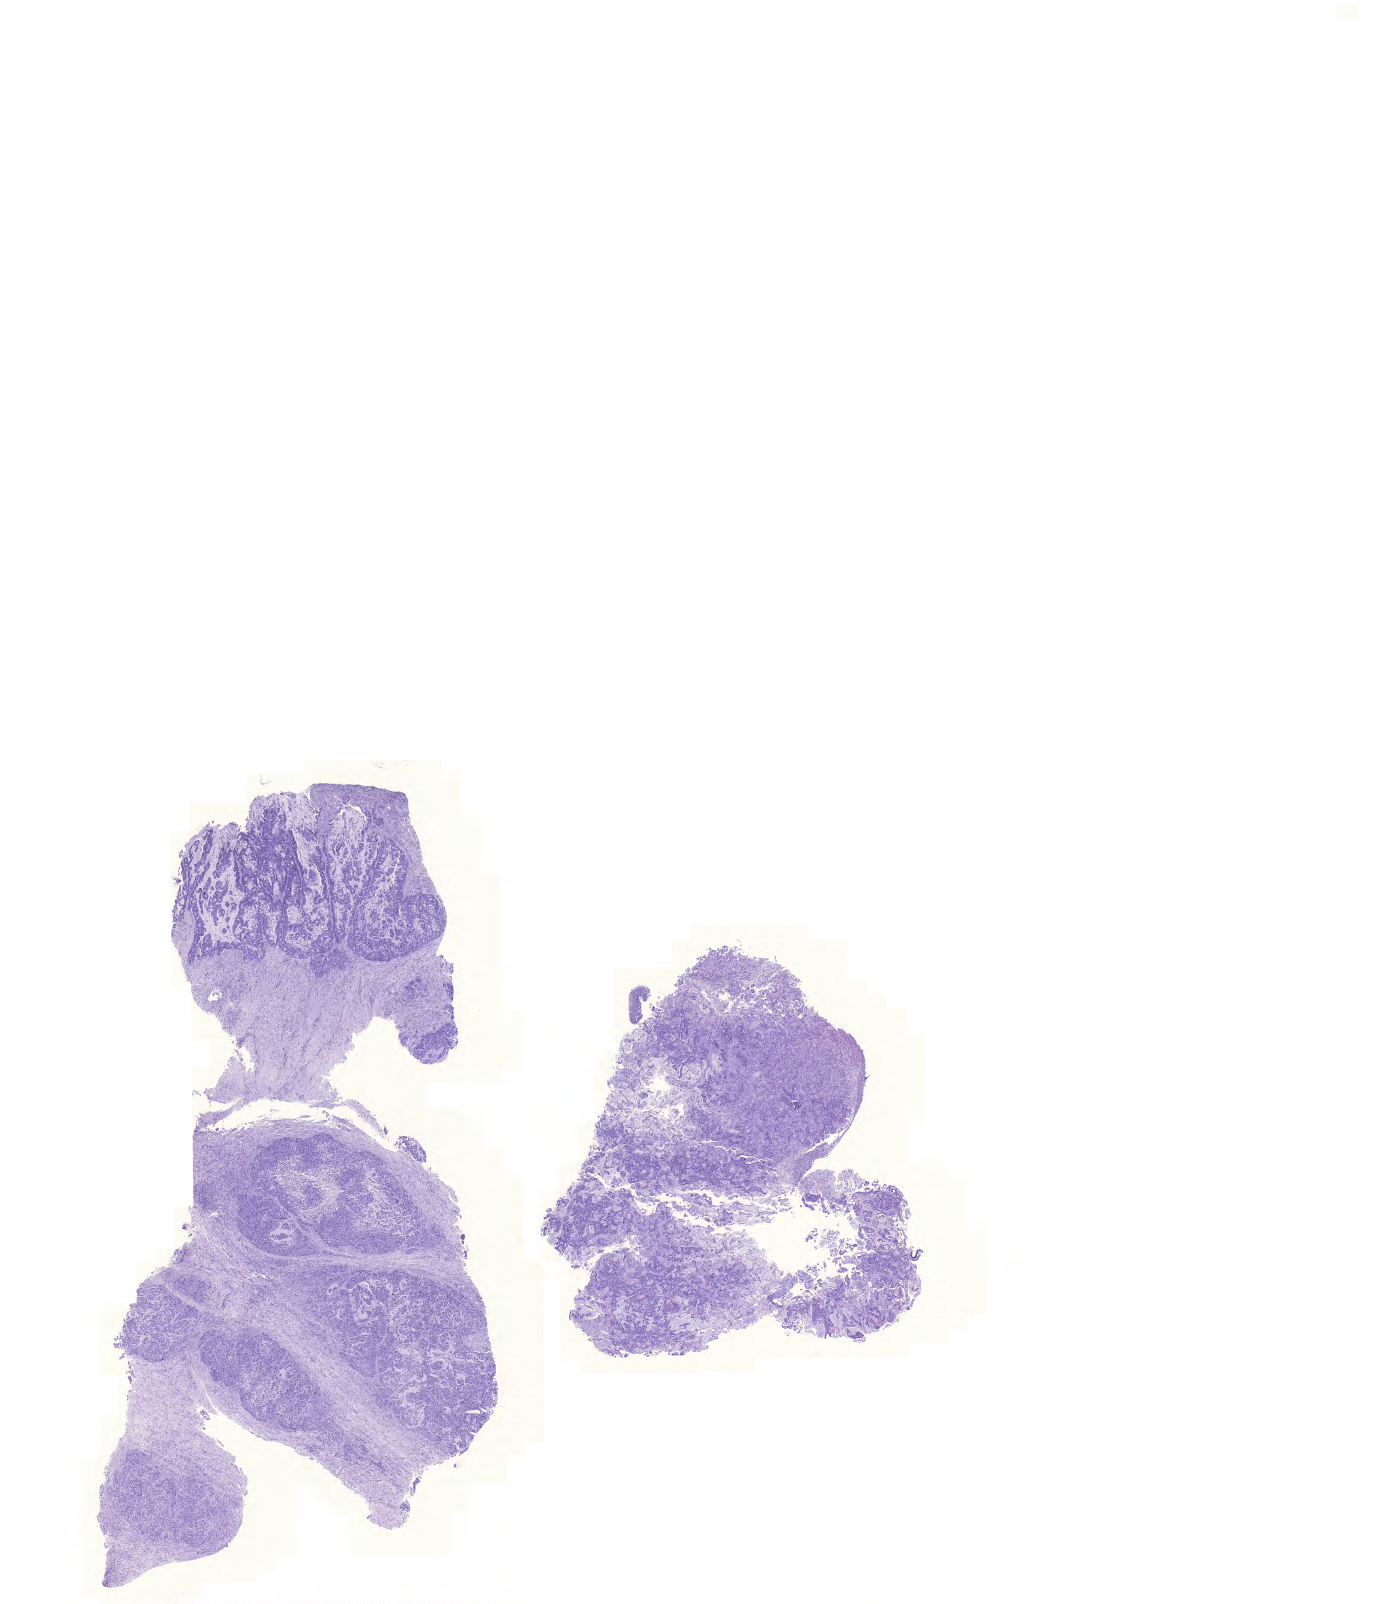
Digitized Hematoxylin and eosin (H&E) stained tissue section (whole slide), low-resolution overview of the scanned area, about 20.5 x 23.9 mm (slide scanned at 20x); FFPE section; colon, primary tumour sample. Female, age 89 years at initial diagnosis.
AJCC pathologic stage: IIA. Pathologic diagnosis: Mucinous adenocarcinoma.